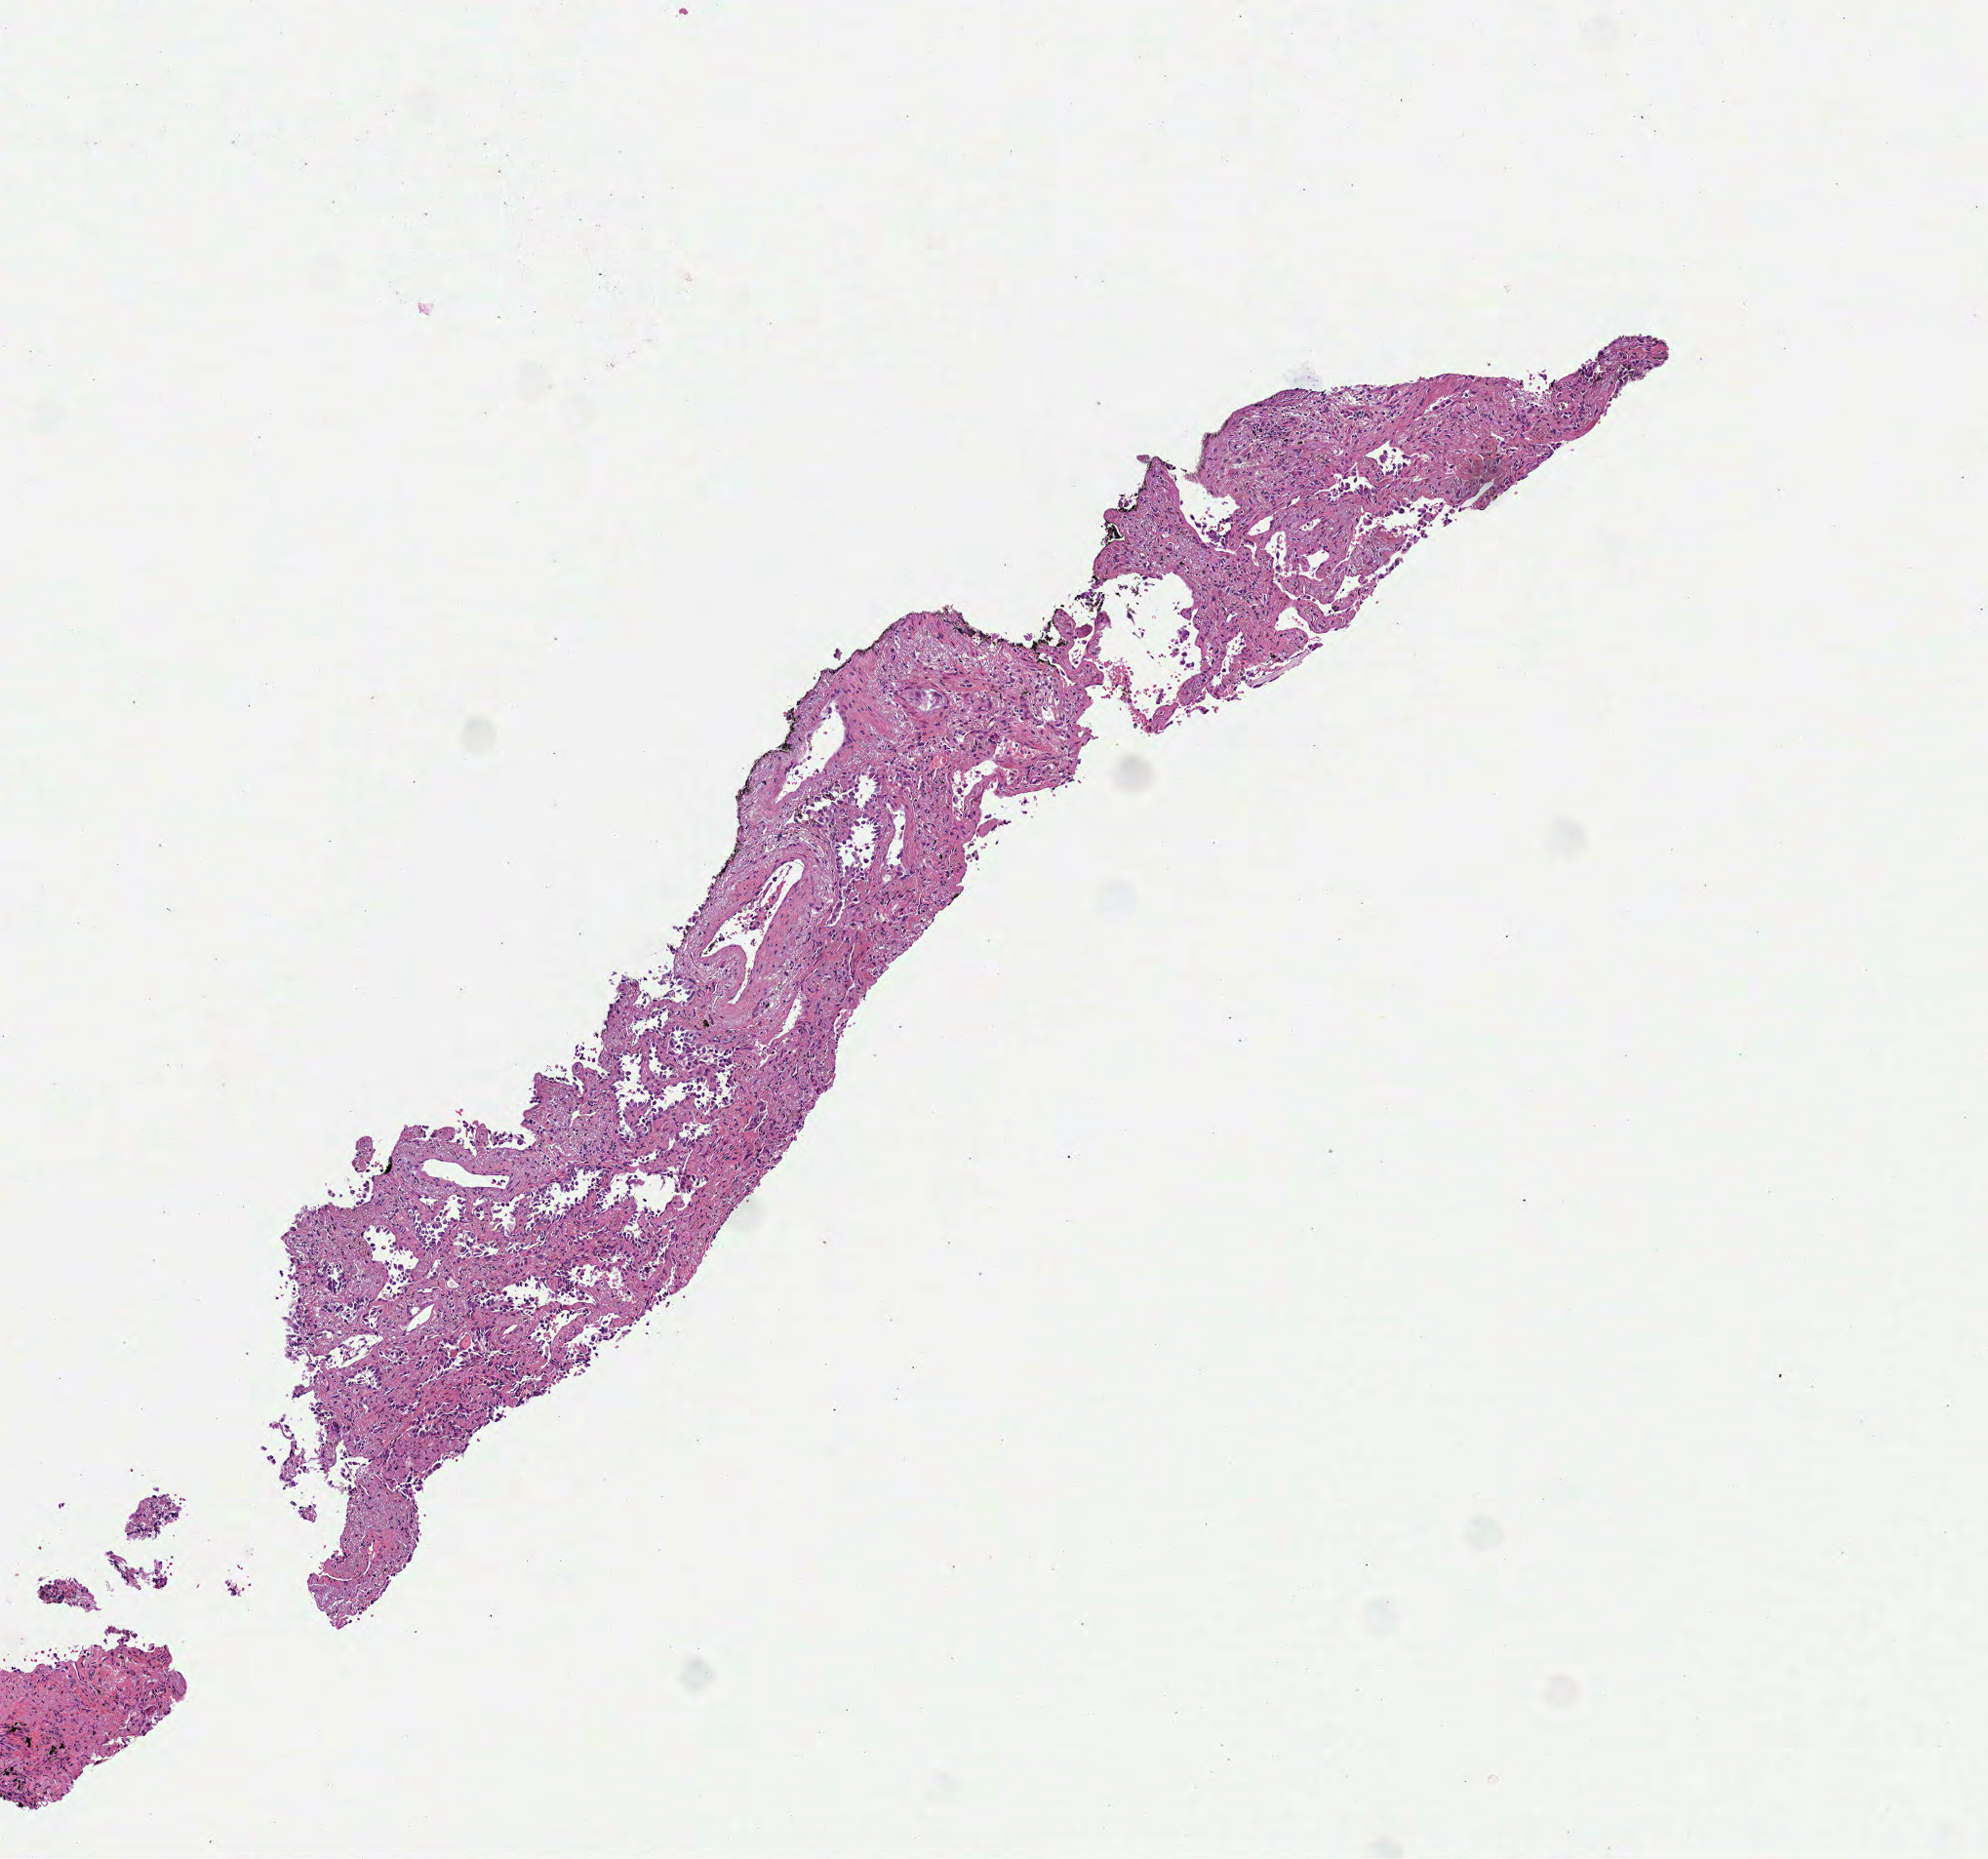
H&E whole-slide image, a low-resolution overview of the entire scanned area, about 4.1 x 3.8 mm (from a 40x scan), formalin-fixed paraffin-embedded (FFPE) diagnostic section, primary tumour sample from the lung. Patient: male, age at initial diagnosis 73 years.
Histologic diagnosis: Acinar cell carcinoma.